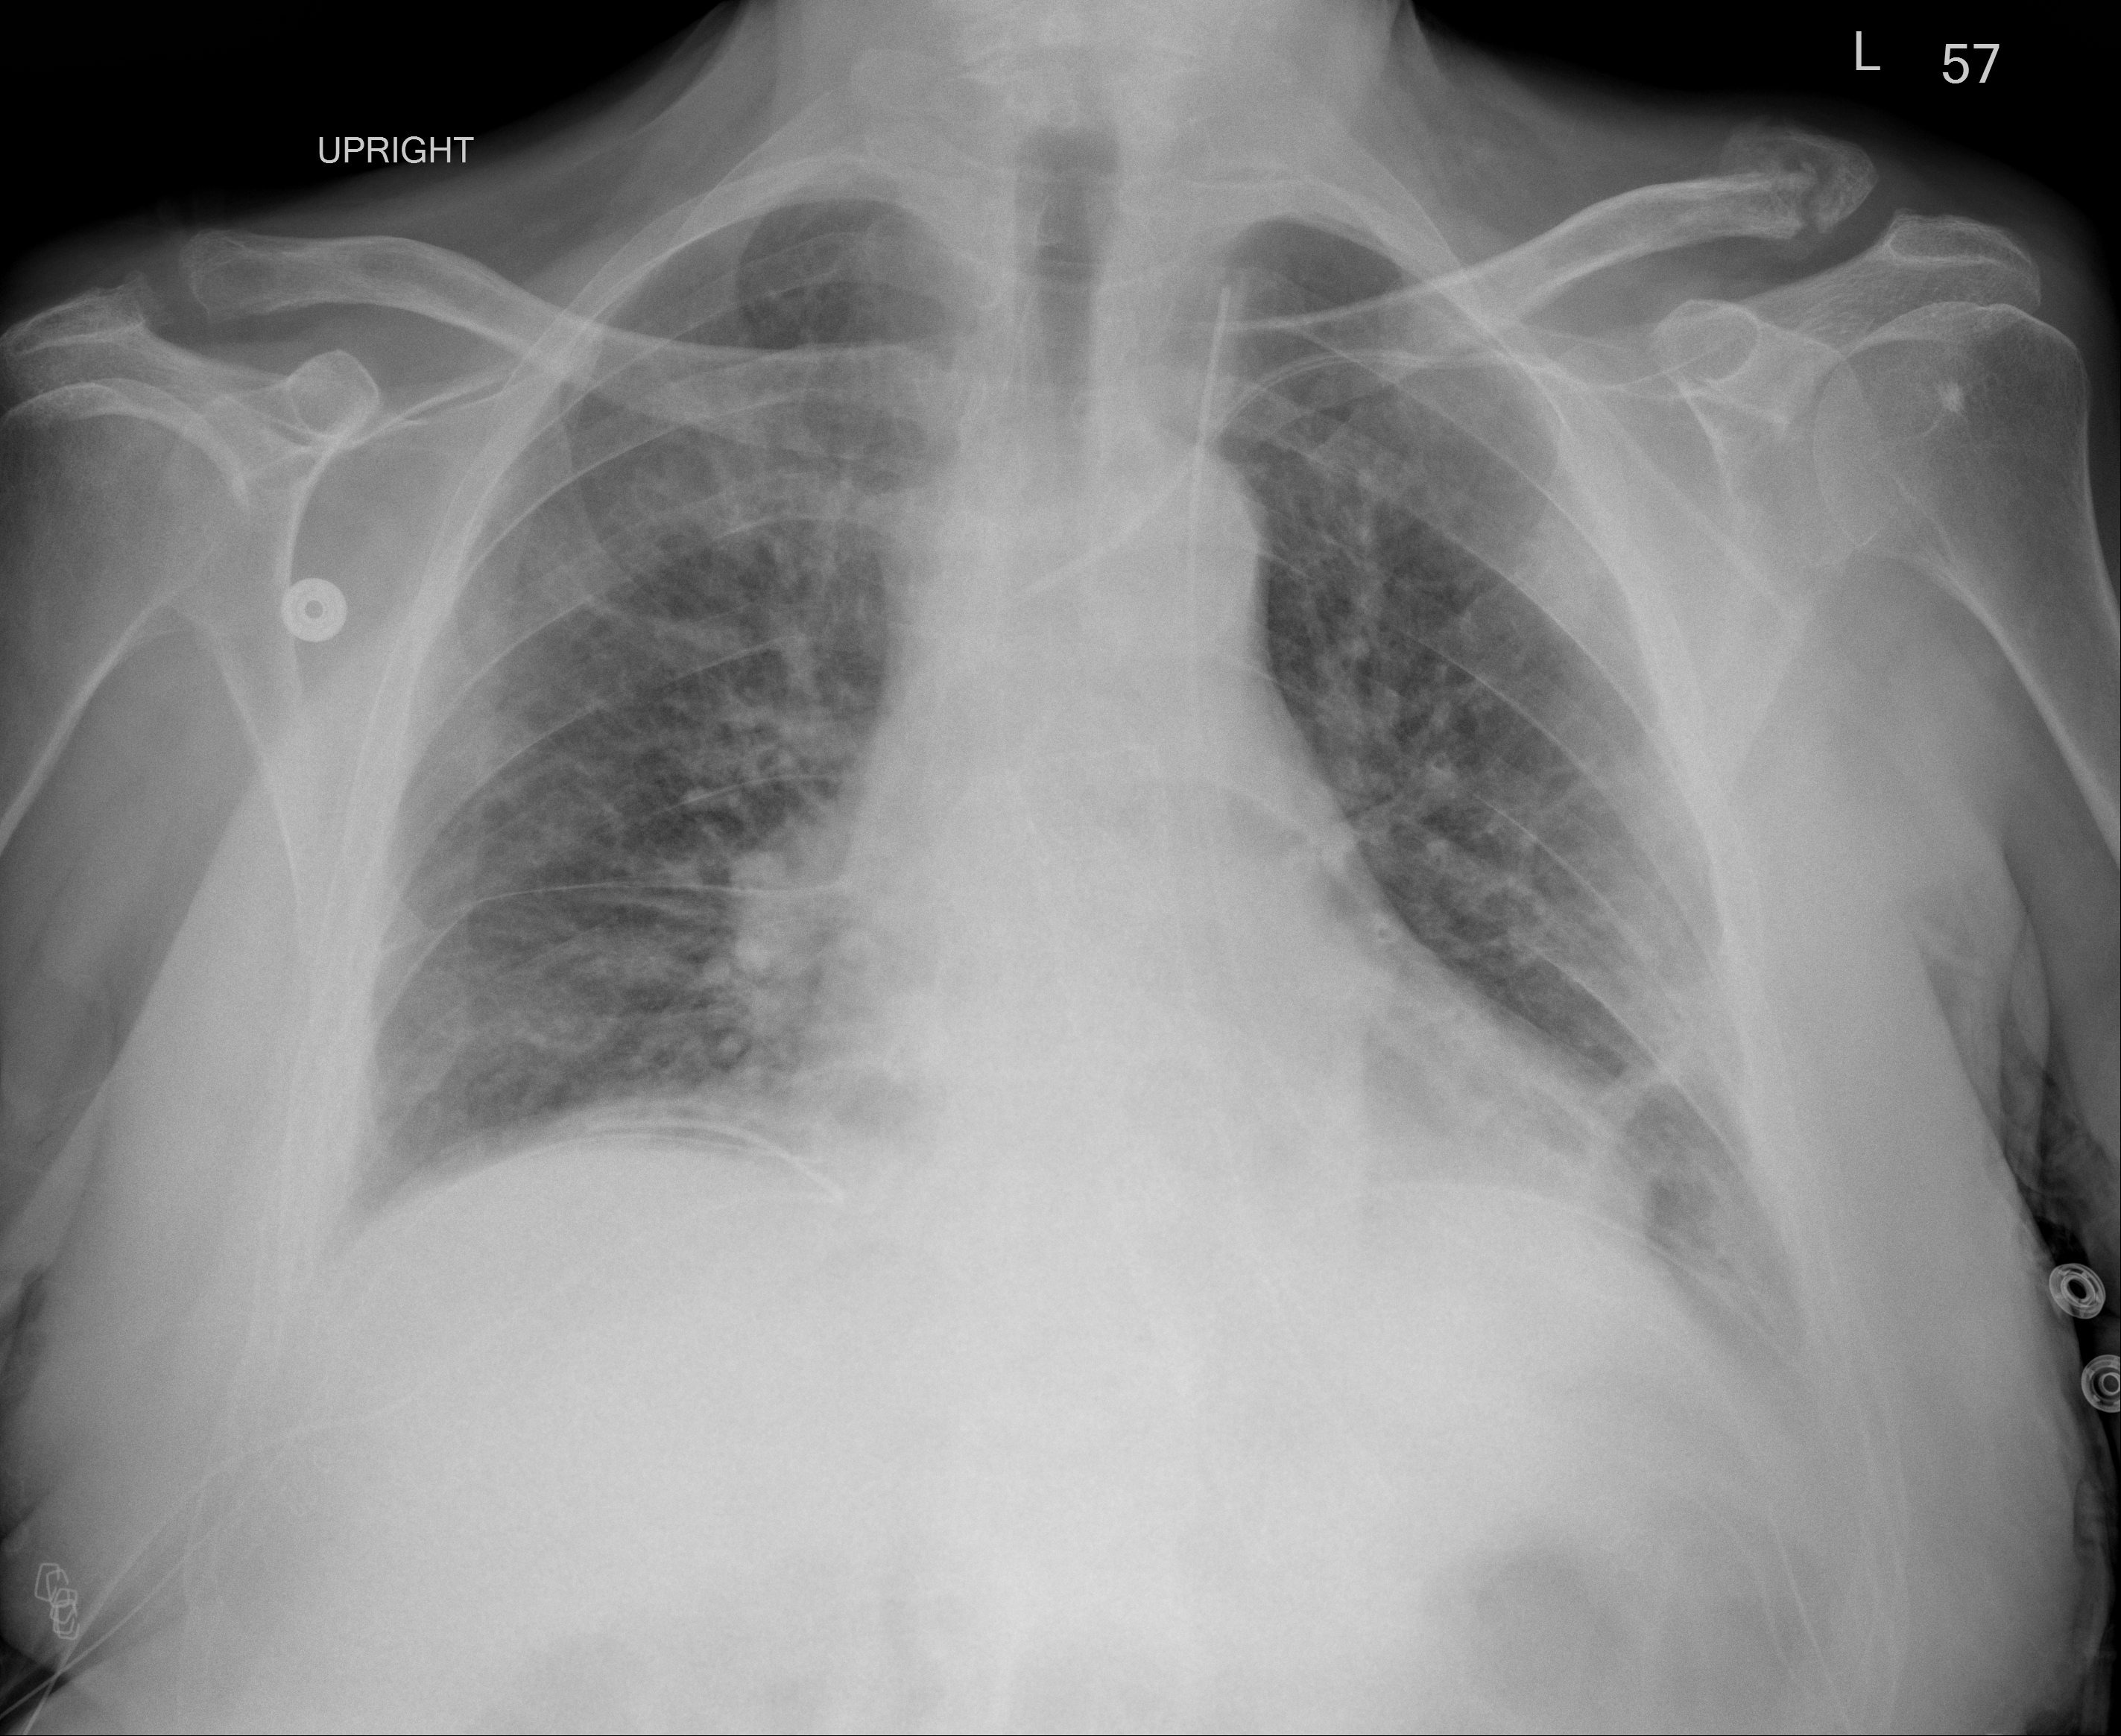
Chest X-ray (portable), AP projection. Male patient, age 64 years; imaged 10 days after the COVID-19 diagnosis.
Key findings recorded by the radiologist: Persistent bibasilar atelectatic changes with probable small left pleural effusion.